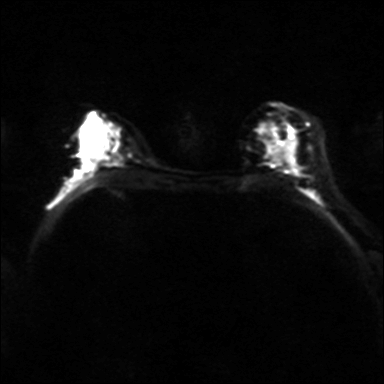
Breast MRI, one axial slice. Diffusion-weighted series; image 2 of 4 stored at this slice position (different b-values; order by instance number). 3 T. 384 × 384 image matrix, field of view 320 × 320 mm. Female patient.
Annotated regions visible in this slice (expert manual segmentation):
- tumour on diffusion-weighted imaging: bounding box <106,126,121,152> (left, top, right, bottom; pixels)